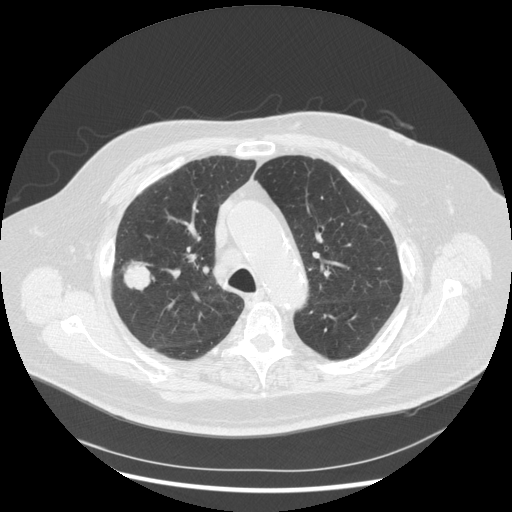
Chest CT (low-dose screening protocol), one axial image; third annual screen; lung window (W 1500 / L -600 HU); standard (soft-tissue) reconstruction kernel (STANDARD); slice 201 of 263 in the series; 512 × 512 image matrix. Male participant, aged 72 years at enrolment. Former smoker at enrolment.
- Expert reader's lesion annotation, box from (x=109, y=251) to (x=163, y=301) px.
- Screening reader's record for this exam (one nodule recorded; not confirmed to be the boxed lesion): non-calcified nodule or mass ≥4 mm, right upper lobe, 31 × 31 mm, poorly defined margins, soft tissue attenuation, pre-existing on the prior screen: no.